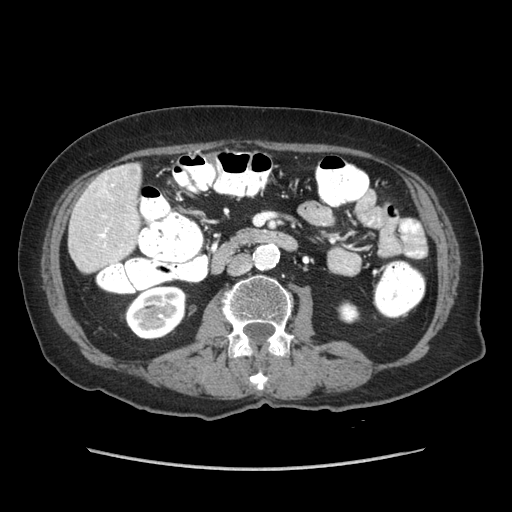
Contrast-enhanced abdominal CT (liver protocol), one axial slice; position 16 of 89 along the scan axis; reconstruction kernel STANDARD; 140 kVp; soft-tissue window (W 400 / L 40 HU); 512 × 512 image matrix, field of view 360 × 360 mm. Case-level facts recorded for this patient, not image findings: diagnosis: hepatocellular carcinoma (patient treated with transarterial chemoembolisation; whether this scan precedes or follows treatment is not stated here); TNM stage (as recorded): Stage-IIIA; Child-Pugh class: A; tumour differentiation: well differentiated; tumour nodularity: multinodular.
Outlined on this slice (semi-automatically segmented with operator editing):
- liver parenchyma outside the tumour (the mass and vessels are separate outlines, so this box may not span the whole liver): bounding box [x1, y1, x2, y2] px = [68, 164, 140, 272]
- liver vessels: [99, 184, 135, 253]